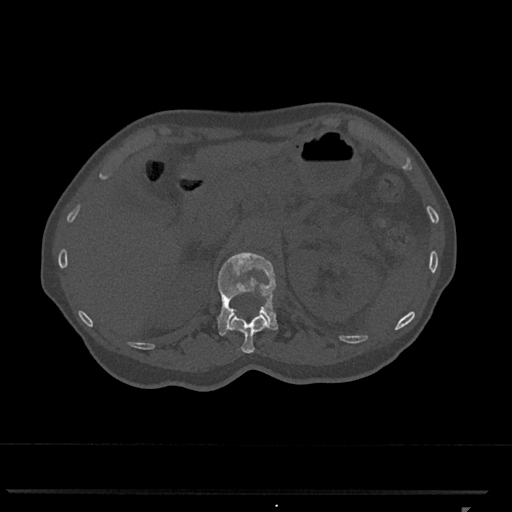
CT including the spine, one axial slice. Position 429 of 793 along the scan axis. Reconstruction kernel Br40s/3. 120 kVp. Bone window (W 1800 / L 400 HU). 0.5 mm slice thickness. 512 × 512 image matrix. Patient: female, 62 years. From the clinical record (not read from this slice): primary cancer: renal.
Structures marked on this image (semi-automatically segmented with operator editing):
- L1 vertebra: box from (x=217, y=252) to (x=278, y=336) px
- T12 vertebra: (x=229, y=312)–(x=268, y=354)